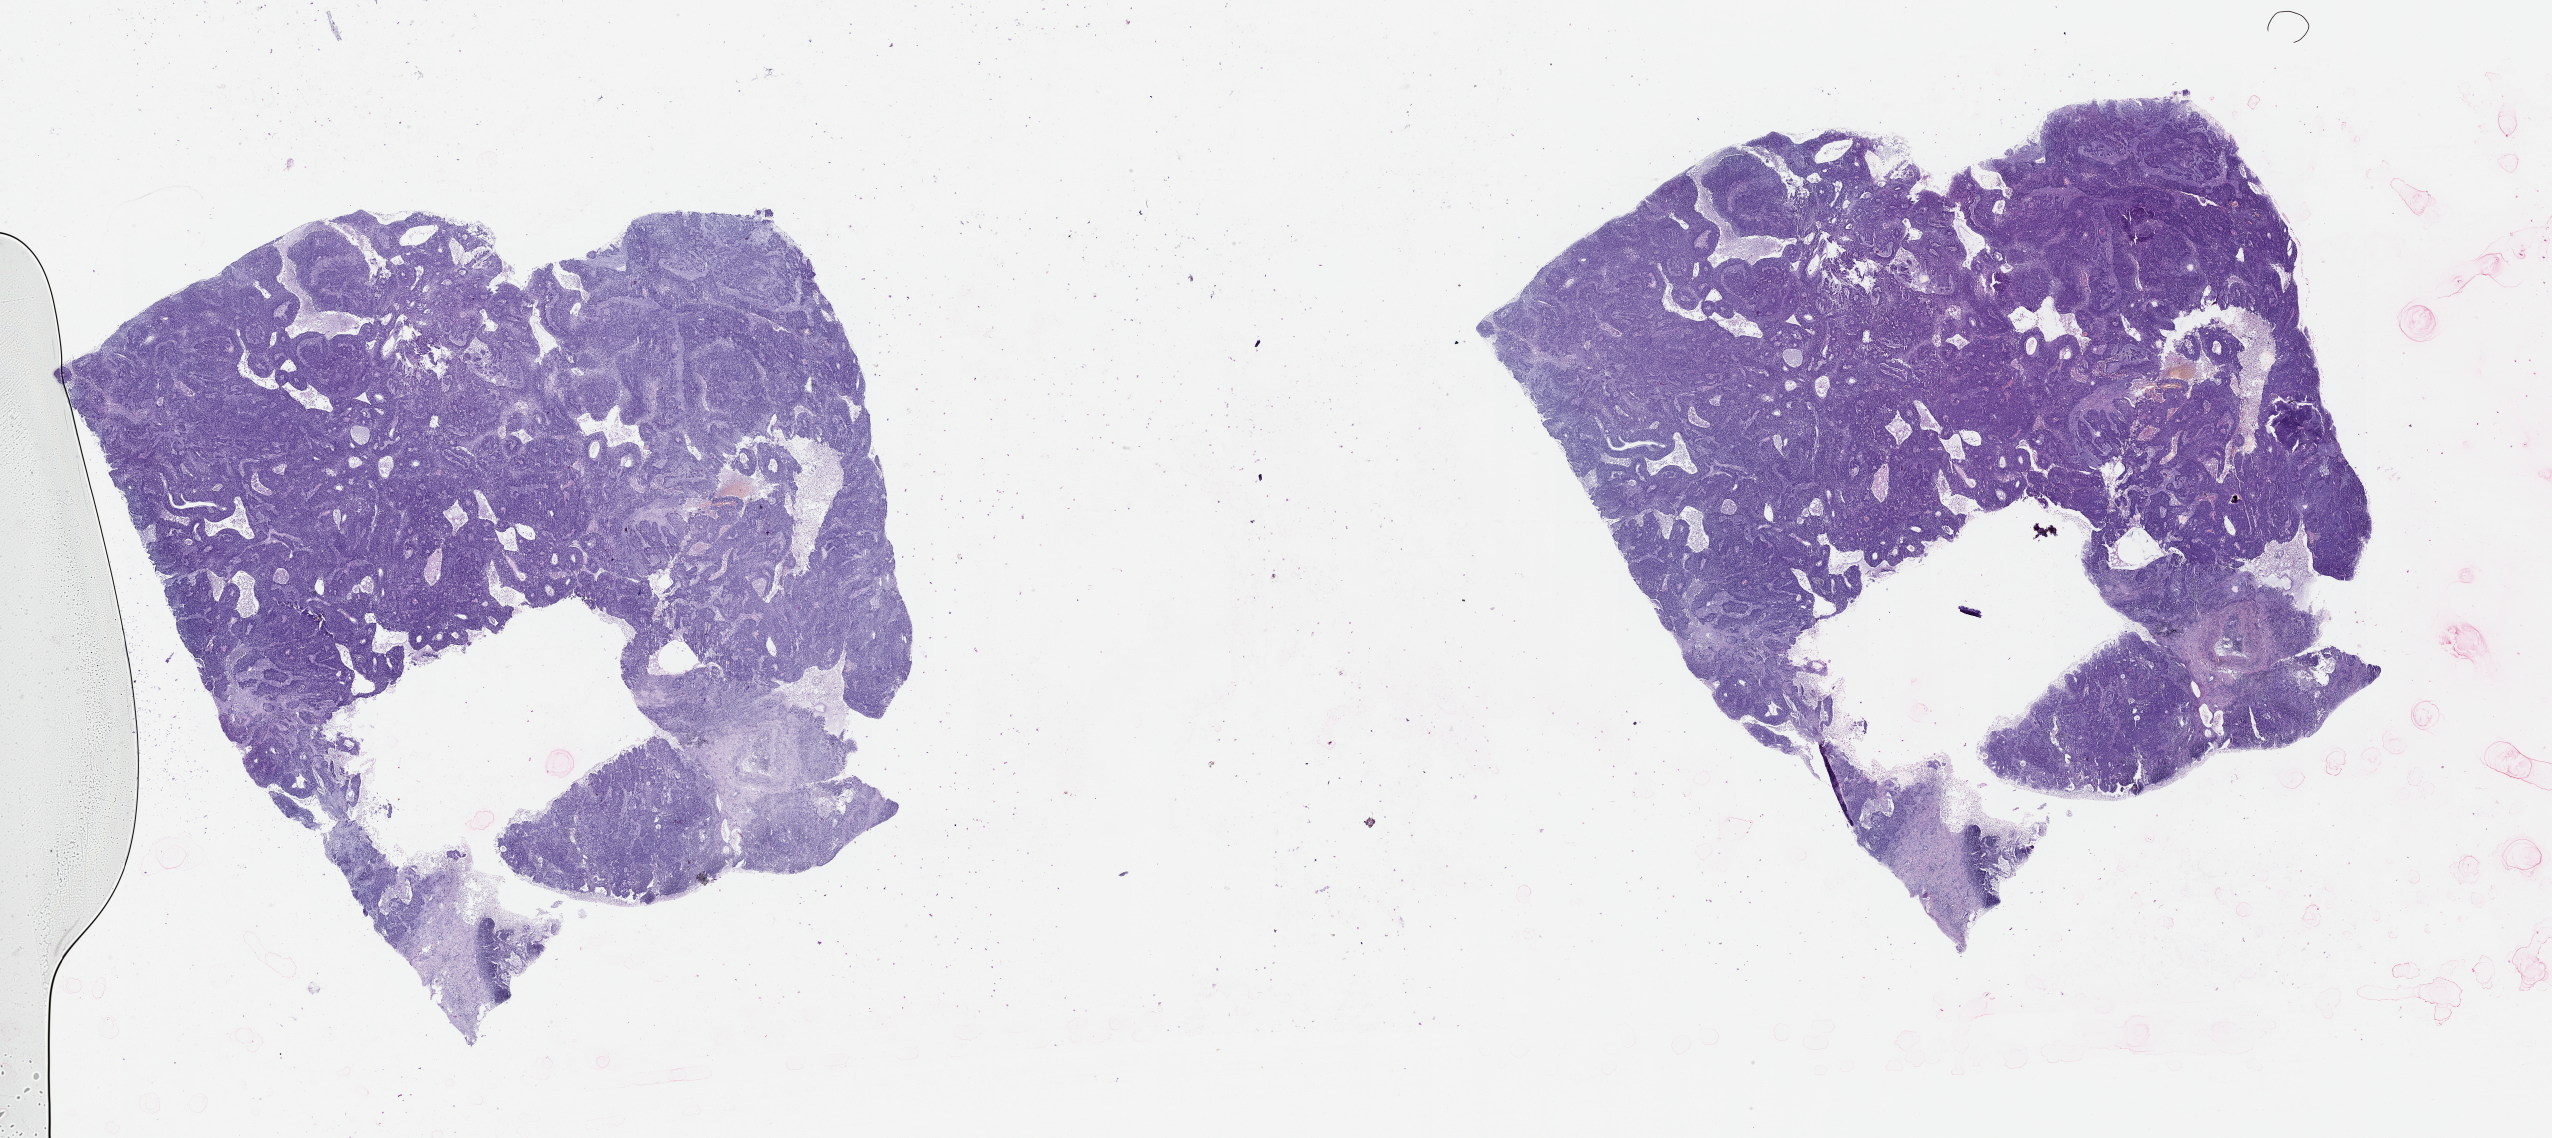
Digitized H&E-stained tissue section (whole slide) — low-resolution overview of the scanned area, about 41.1 x 18.3 mm (slide scanned at 20x). Lung, tumour tissue. 62-year-old female patient.
• patient diagnosis (cohort enrolment): squamous cell carcinoma (lung)